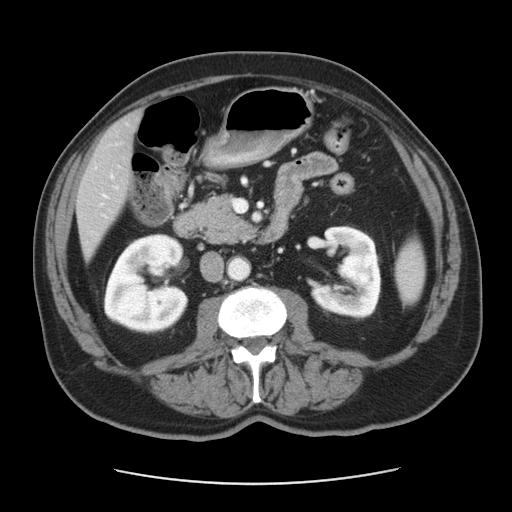
Contrast-enhanced abdominal CT, one axial slice; position 16 of 42 along the scan axis; reconstruction kernel STANDARD; 120 kVp; intravenous contrast given; soft-tissue window (W 400 / L 40 HU); 5 mm slice thickness; 512 × 512 image matrix, field of view 370 × 370 mm. Male patient, age 73 years. From the clinical record (not read from this slice): diagnosis: colorectal cancer liver metastases, imaged before liver resection; multiple liver metastases: yes; largest metastasis: 0.5 cm; disease in both lobes: no.
Structures marked on this image (outlined manually by an expert reader):
- liver: box from (x=78, y=113) to (x=139, y=255) px
- planned liver remnant (the part of the liver to remain after resection): (x=105, y=113)–(x=139, y=150)